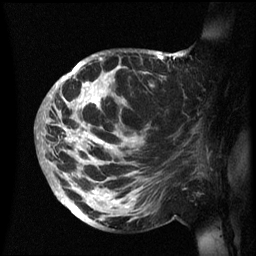
Breast MRI (dynamic contrast-enhanced), one sagittal slice. Slice 36 of 60 in the series (ordered by position). Dynamic contrast-enhanced series, image 2 of 3 at this slice position (ordered by acquisition). 1.5 T. TE 4.2 ms, TR 8.4 ms. 2.4 mm slice thickness. 256 × 256 image matrix. Female patient, age 48 years.
Annotated regions visible in this slice (semi-automatic segmentation, software-assisted and operator-edited):
- analysis volume of interest (the breast-tissue region the enhancement analysis was run in; not a lesion): bounding box [x1, y1, x2, y2] px = [42, 51, 186, 230]
- tumour enhancement mask (voxels above the 70 % enhancement threshold inside the analysis volume of interest): [42, 54, 178, 216]